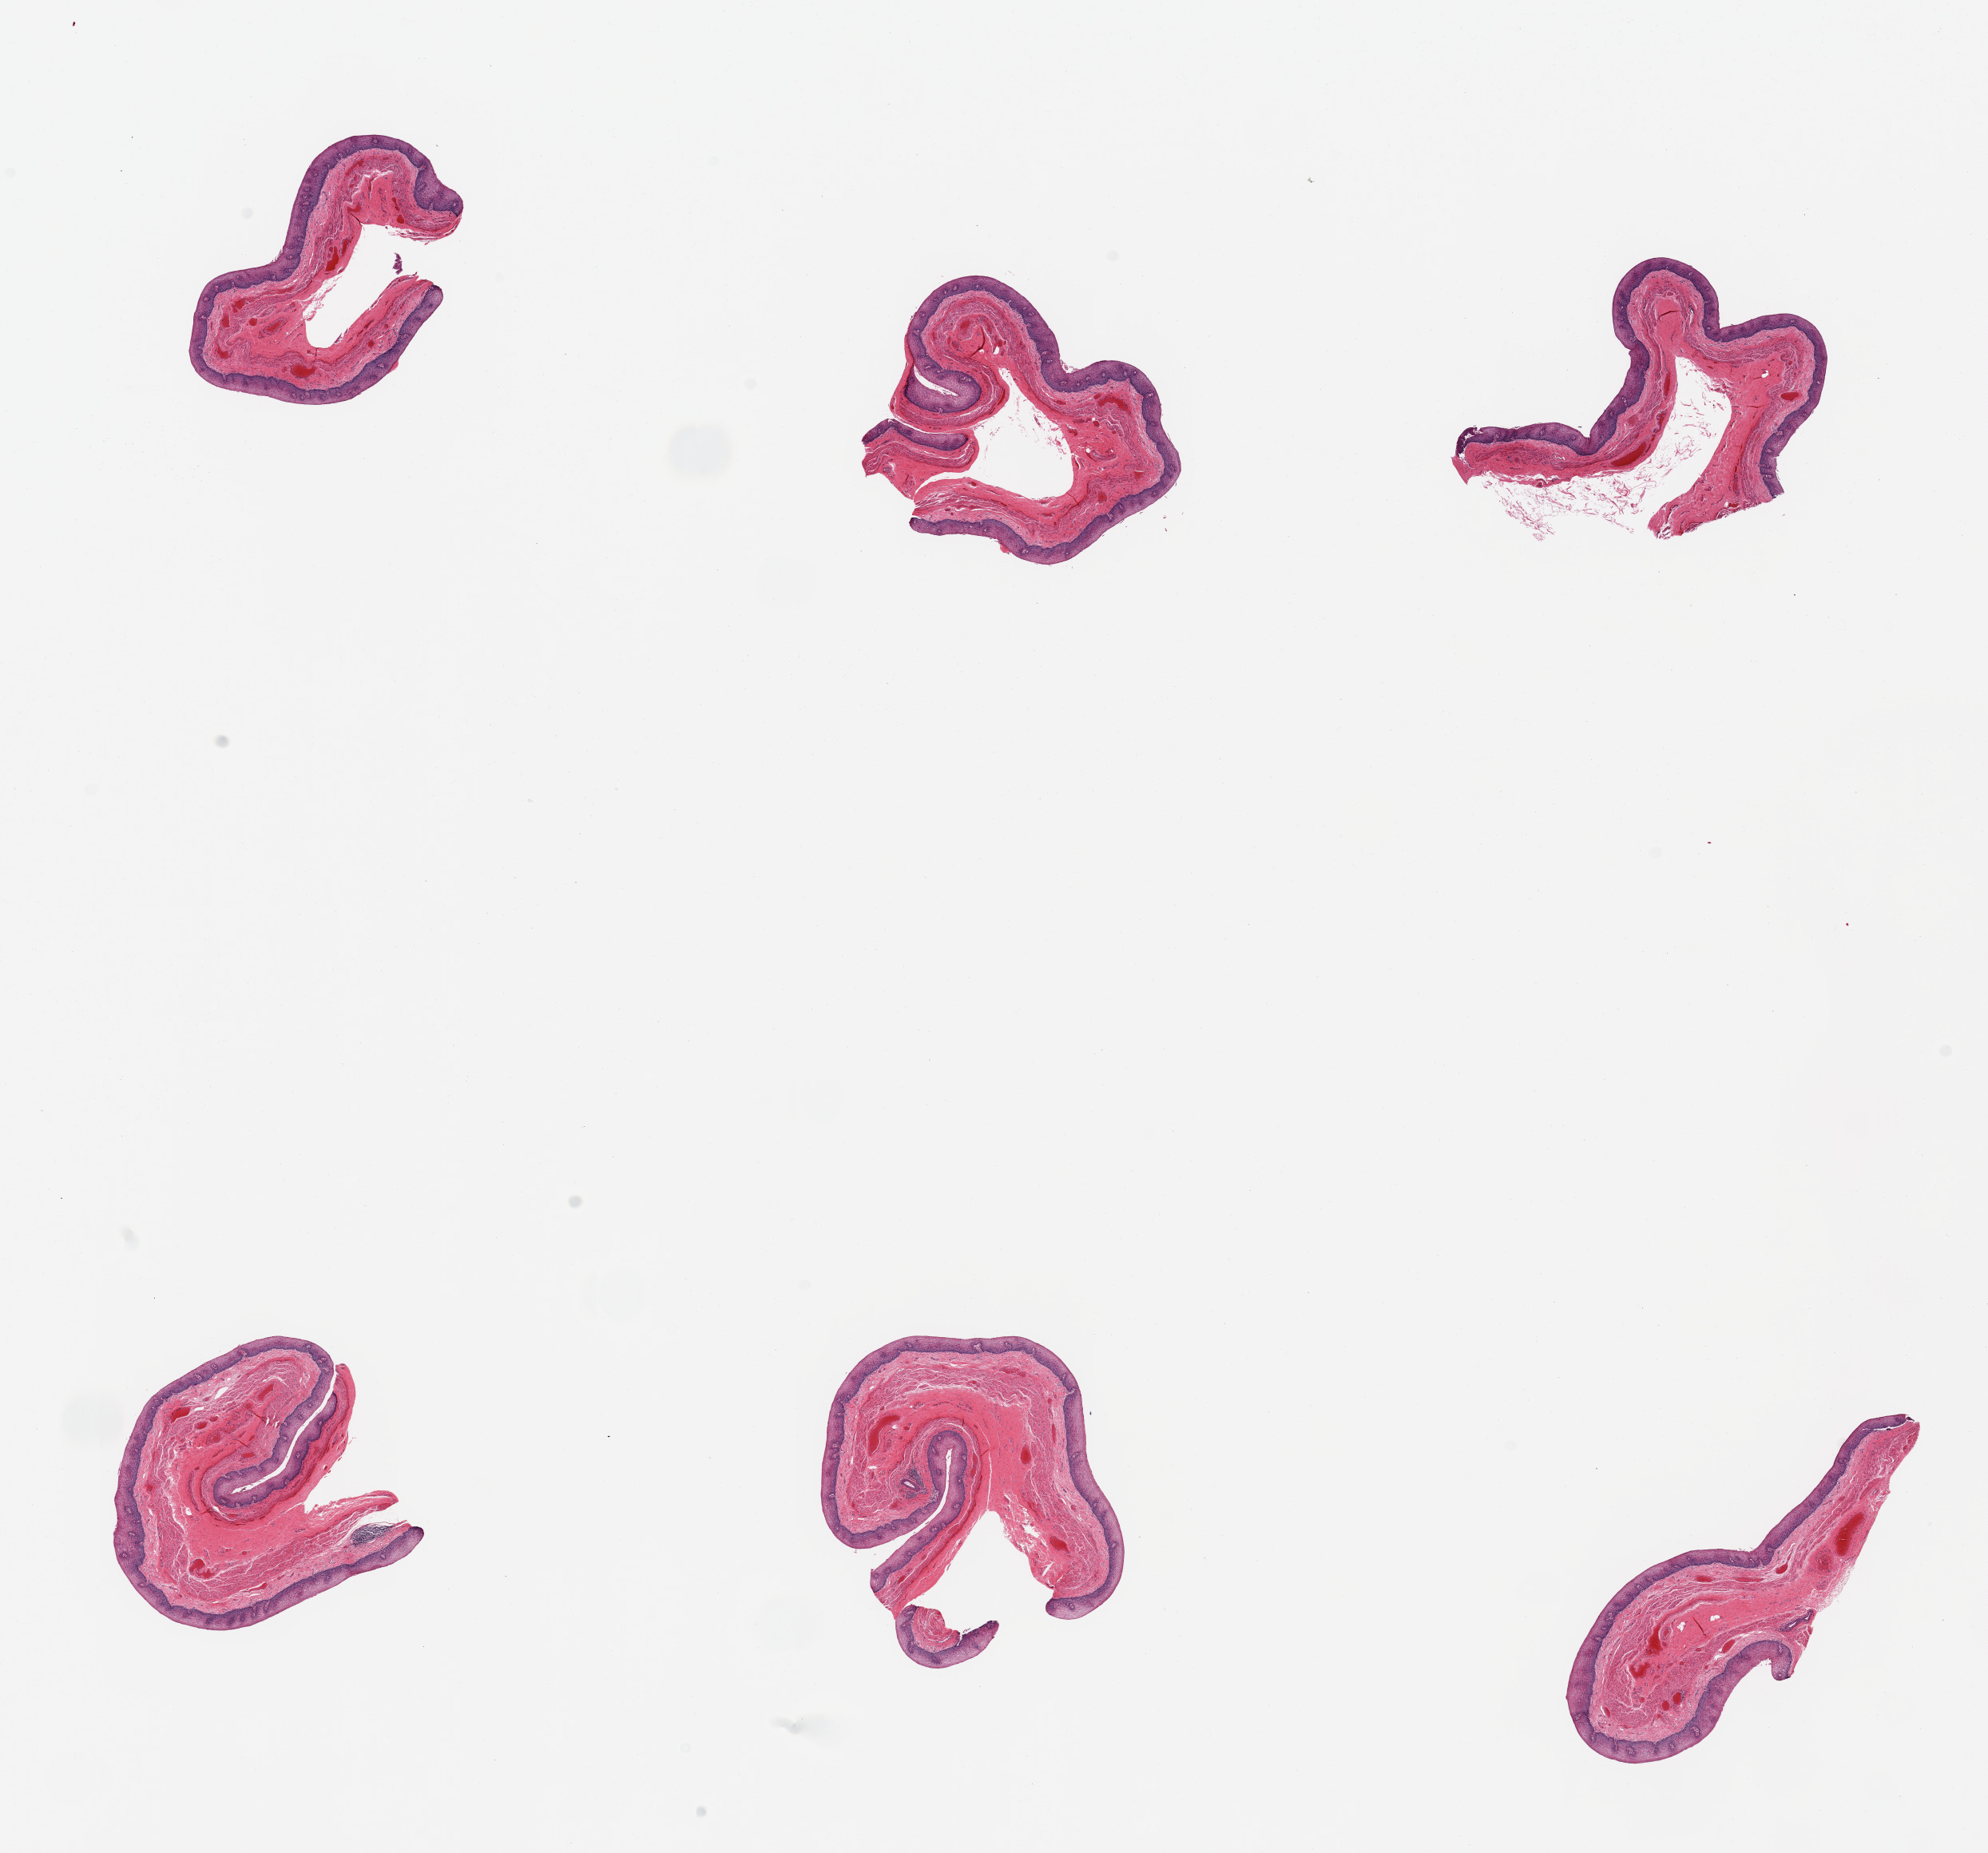
Haematoxylin and eosin whole-slide image — low-resolution overview of the scanned area, about 19.7 x 18.4 mm (acquisition: 20x scan); PAXgene-fixed paraffin-embedded (PFPE) section; target tissue: esophageal mucous membrane; tissue donor sample. Donor: female.
Reviewer comment on this tissue sample: 6 pieces, squamous mucosa up to ~0.3mm thick.